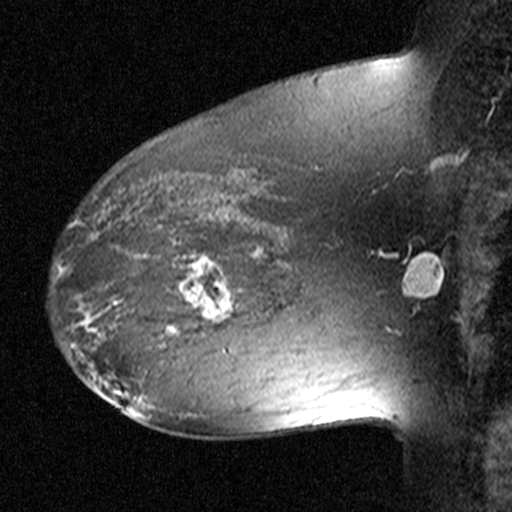
Breast MRI (dynamic contrast-enhanced), one sagittal slice; position 30 of 44 along the scan axis; dynamic contrast-enhanced study with each time point stored as its own series, time point 2 of 3 at this slice position (early post-contrast, ordered by acquisition time); 1.5 T; TE 4.5 ms, TR 11 ms; 3 mm slice thickness; 512 × 512 image matrix. Patient: female, 38 years. From the clinical record (not read from this slice): setting: breast cancer imaged before/during neoadjuvant chemotherapy; receptor status: HR-positive, HER2-negative.
Structures marked on this image (semi-automatic segmentation, software-assisted and operator-edited):
- analysis volume of interest (the breast-tissue region the enhancement analysis was run in; not a lesion): bounding box [x1, y1, x2, y2] px = [152, 236, 253, 335]
- tumour enhancement mask (voxels above the 90 % enhancement threshold inside the analysis volume of interest): [167, 252, 253, 333]